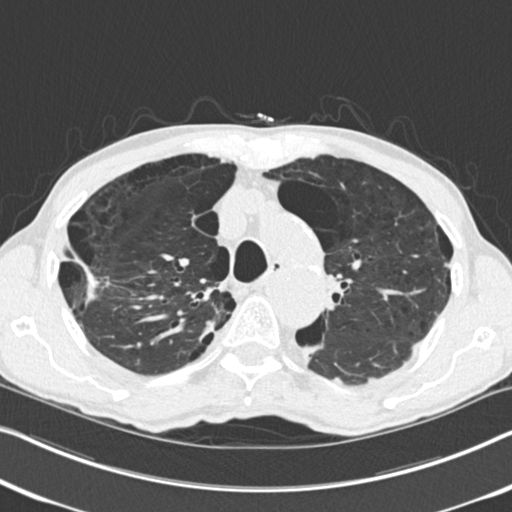
Chest CT (low-dose screening protocol), one axial image; second screening round (one year after baseline); lung window (W 1500 / L -600 HU); standard (soft-tissue) reconstruction kernel (B30f); 120 kVp; slice 70 of 251 in the series; 512 × 512 image matrix. Male participant, aged 71 years at enrolment. Current smoker at enrolment.
Expert-annotated lung lesion, bounding box <52,236,123,316> (left, top, right, bottom; pixels). The screening reader recorded 4 non-calcified nodules or masses ≥4 mm on this exam; which of them this box marks is not recorded.